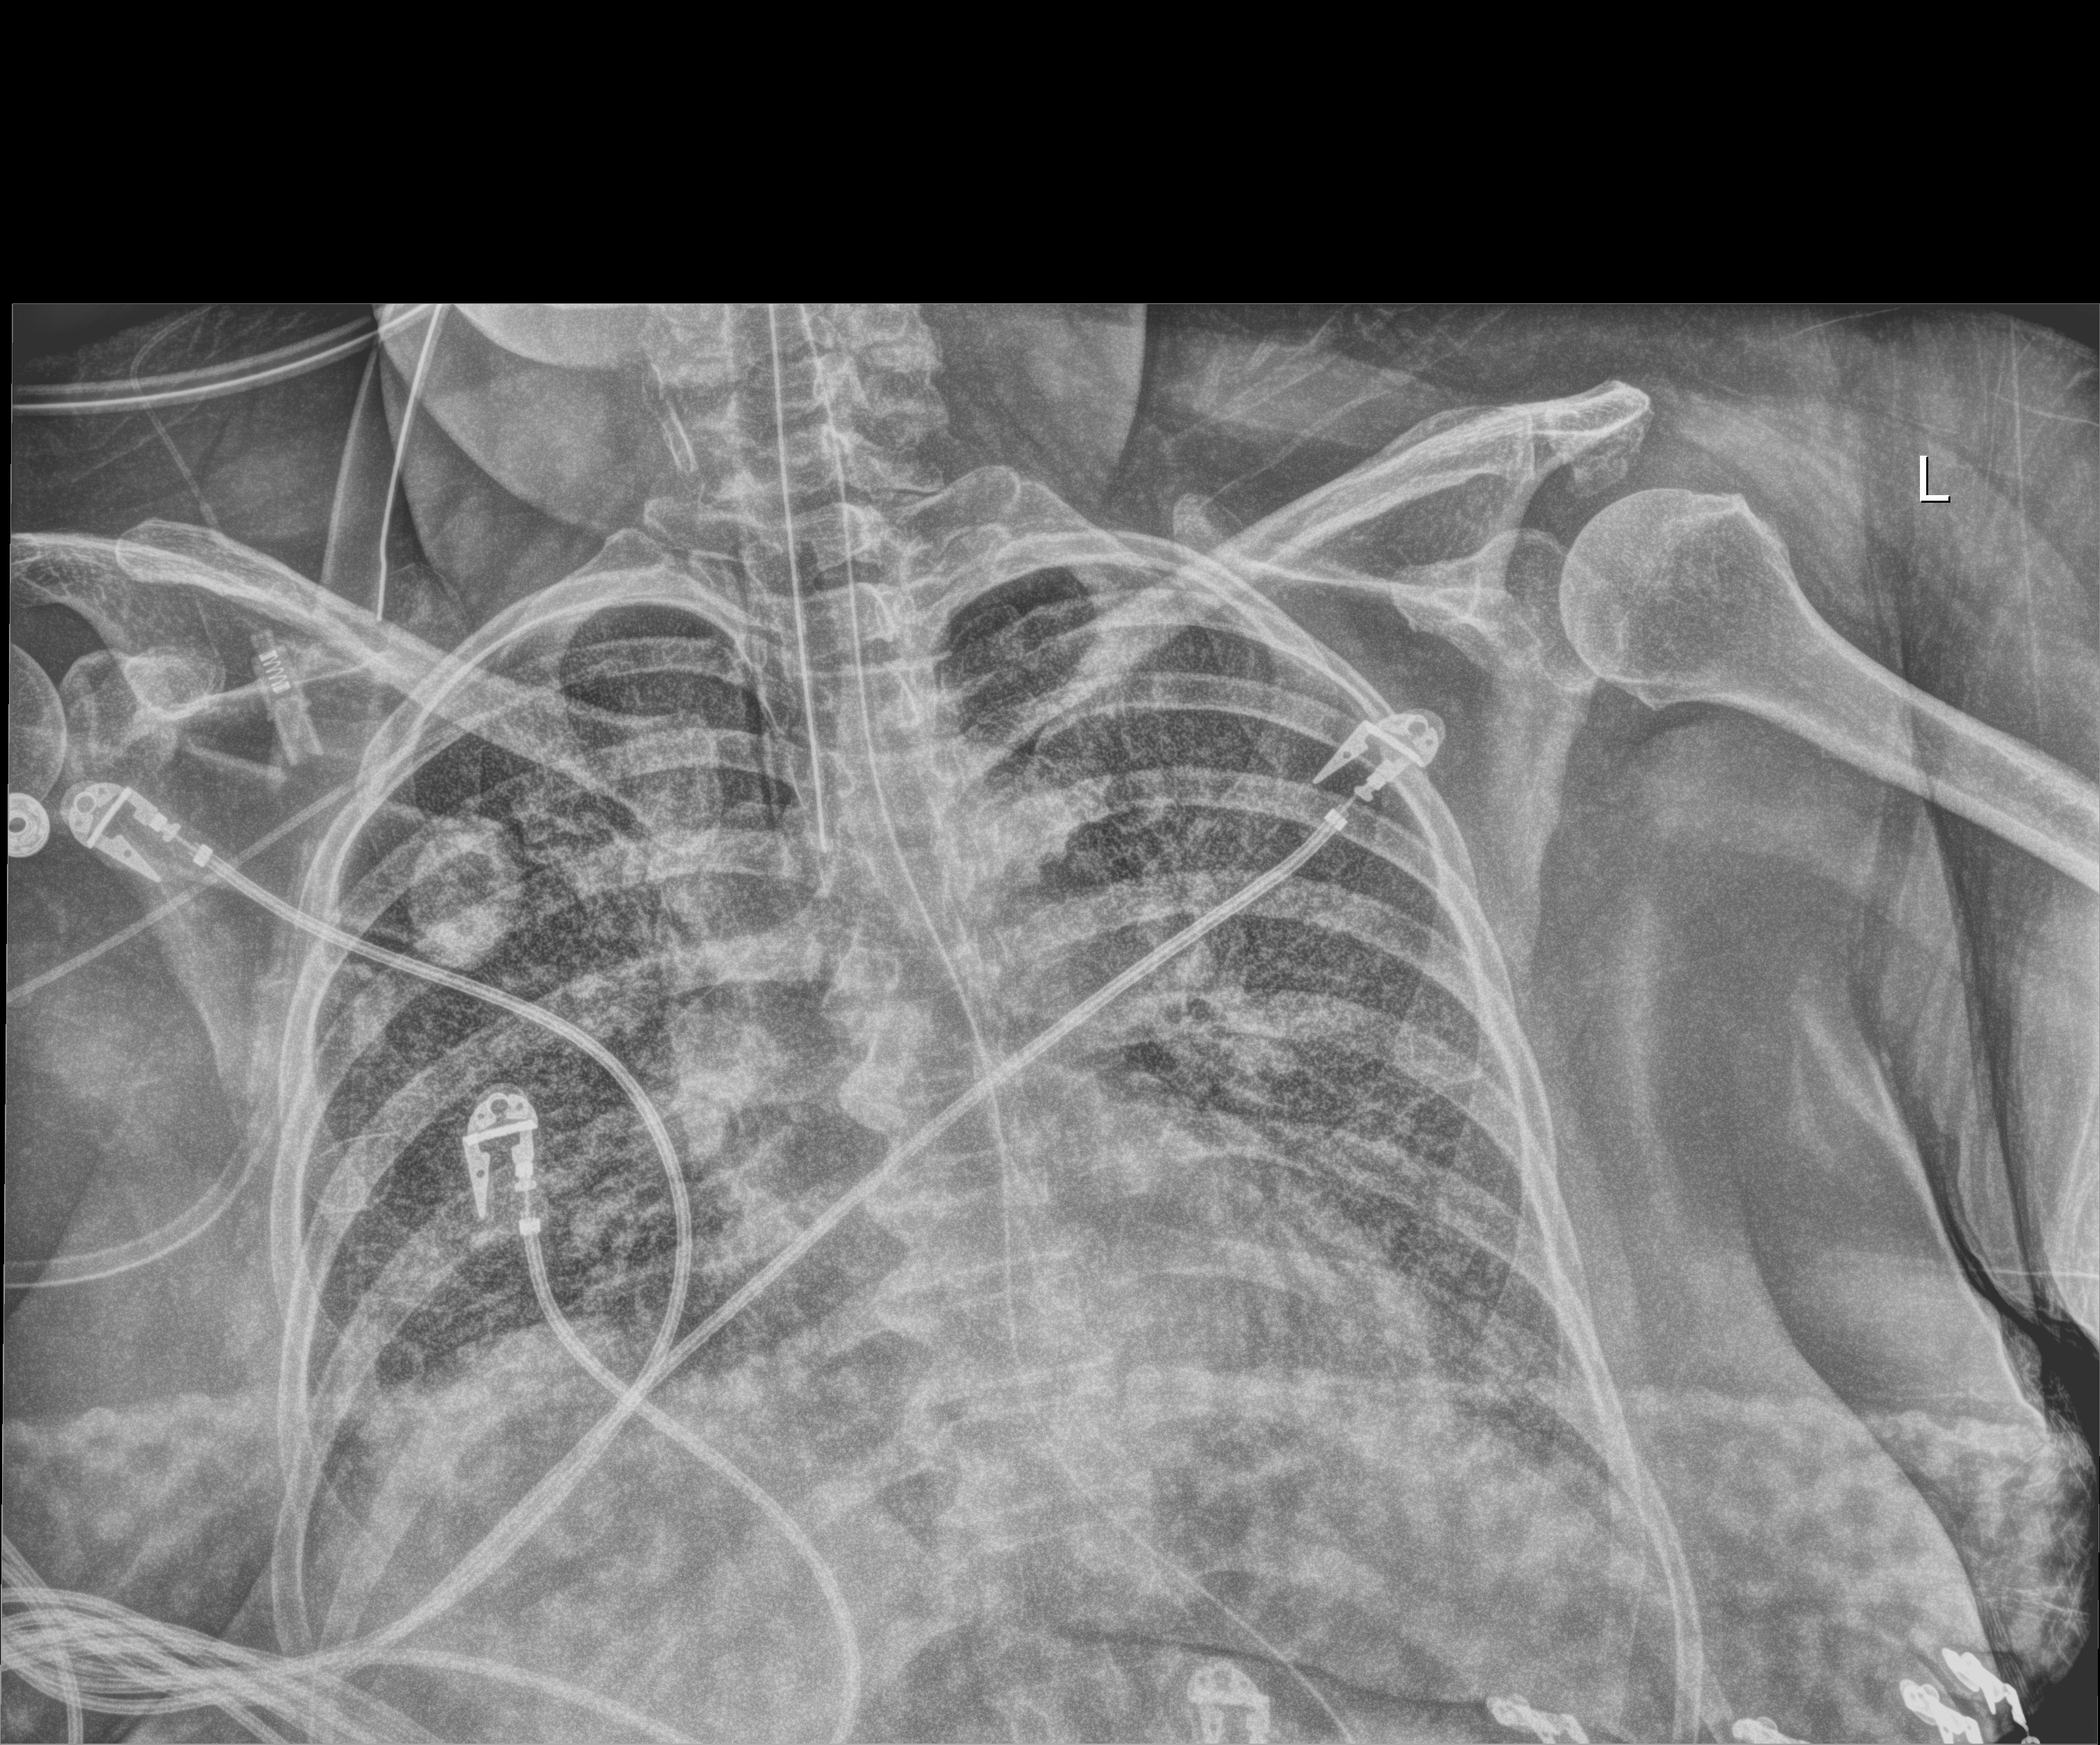
Chest X-ray, anteroposterior (AP) projection. Patient hospitalised with COVID-19; female, aged 60–74 years.
Admission-level facts for this patient (not findings on this image; timing relative to this image not recorded): smoking status (admission record): former; admitted to intensive care during this hospital stay: yes; mechanically ventilated during this hospital stay: yes.